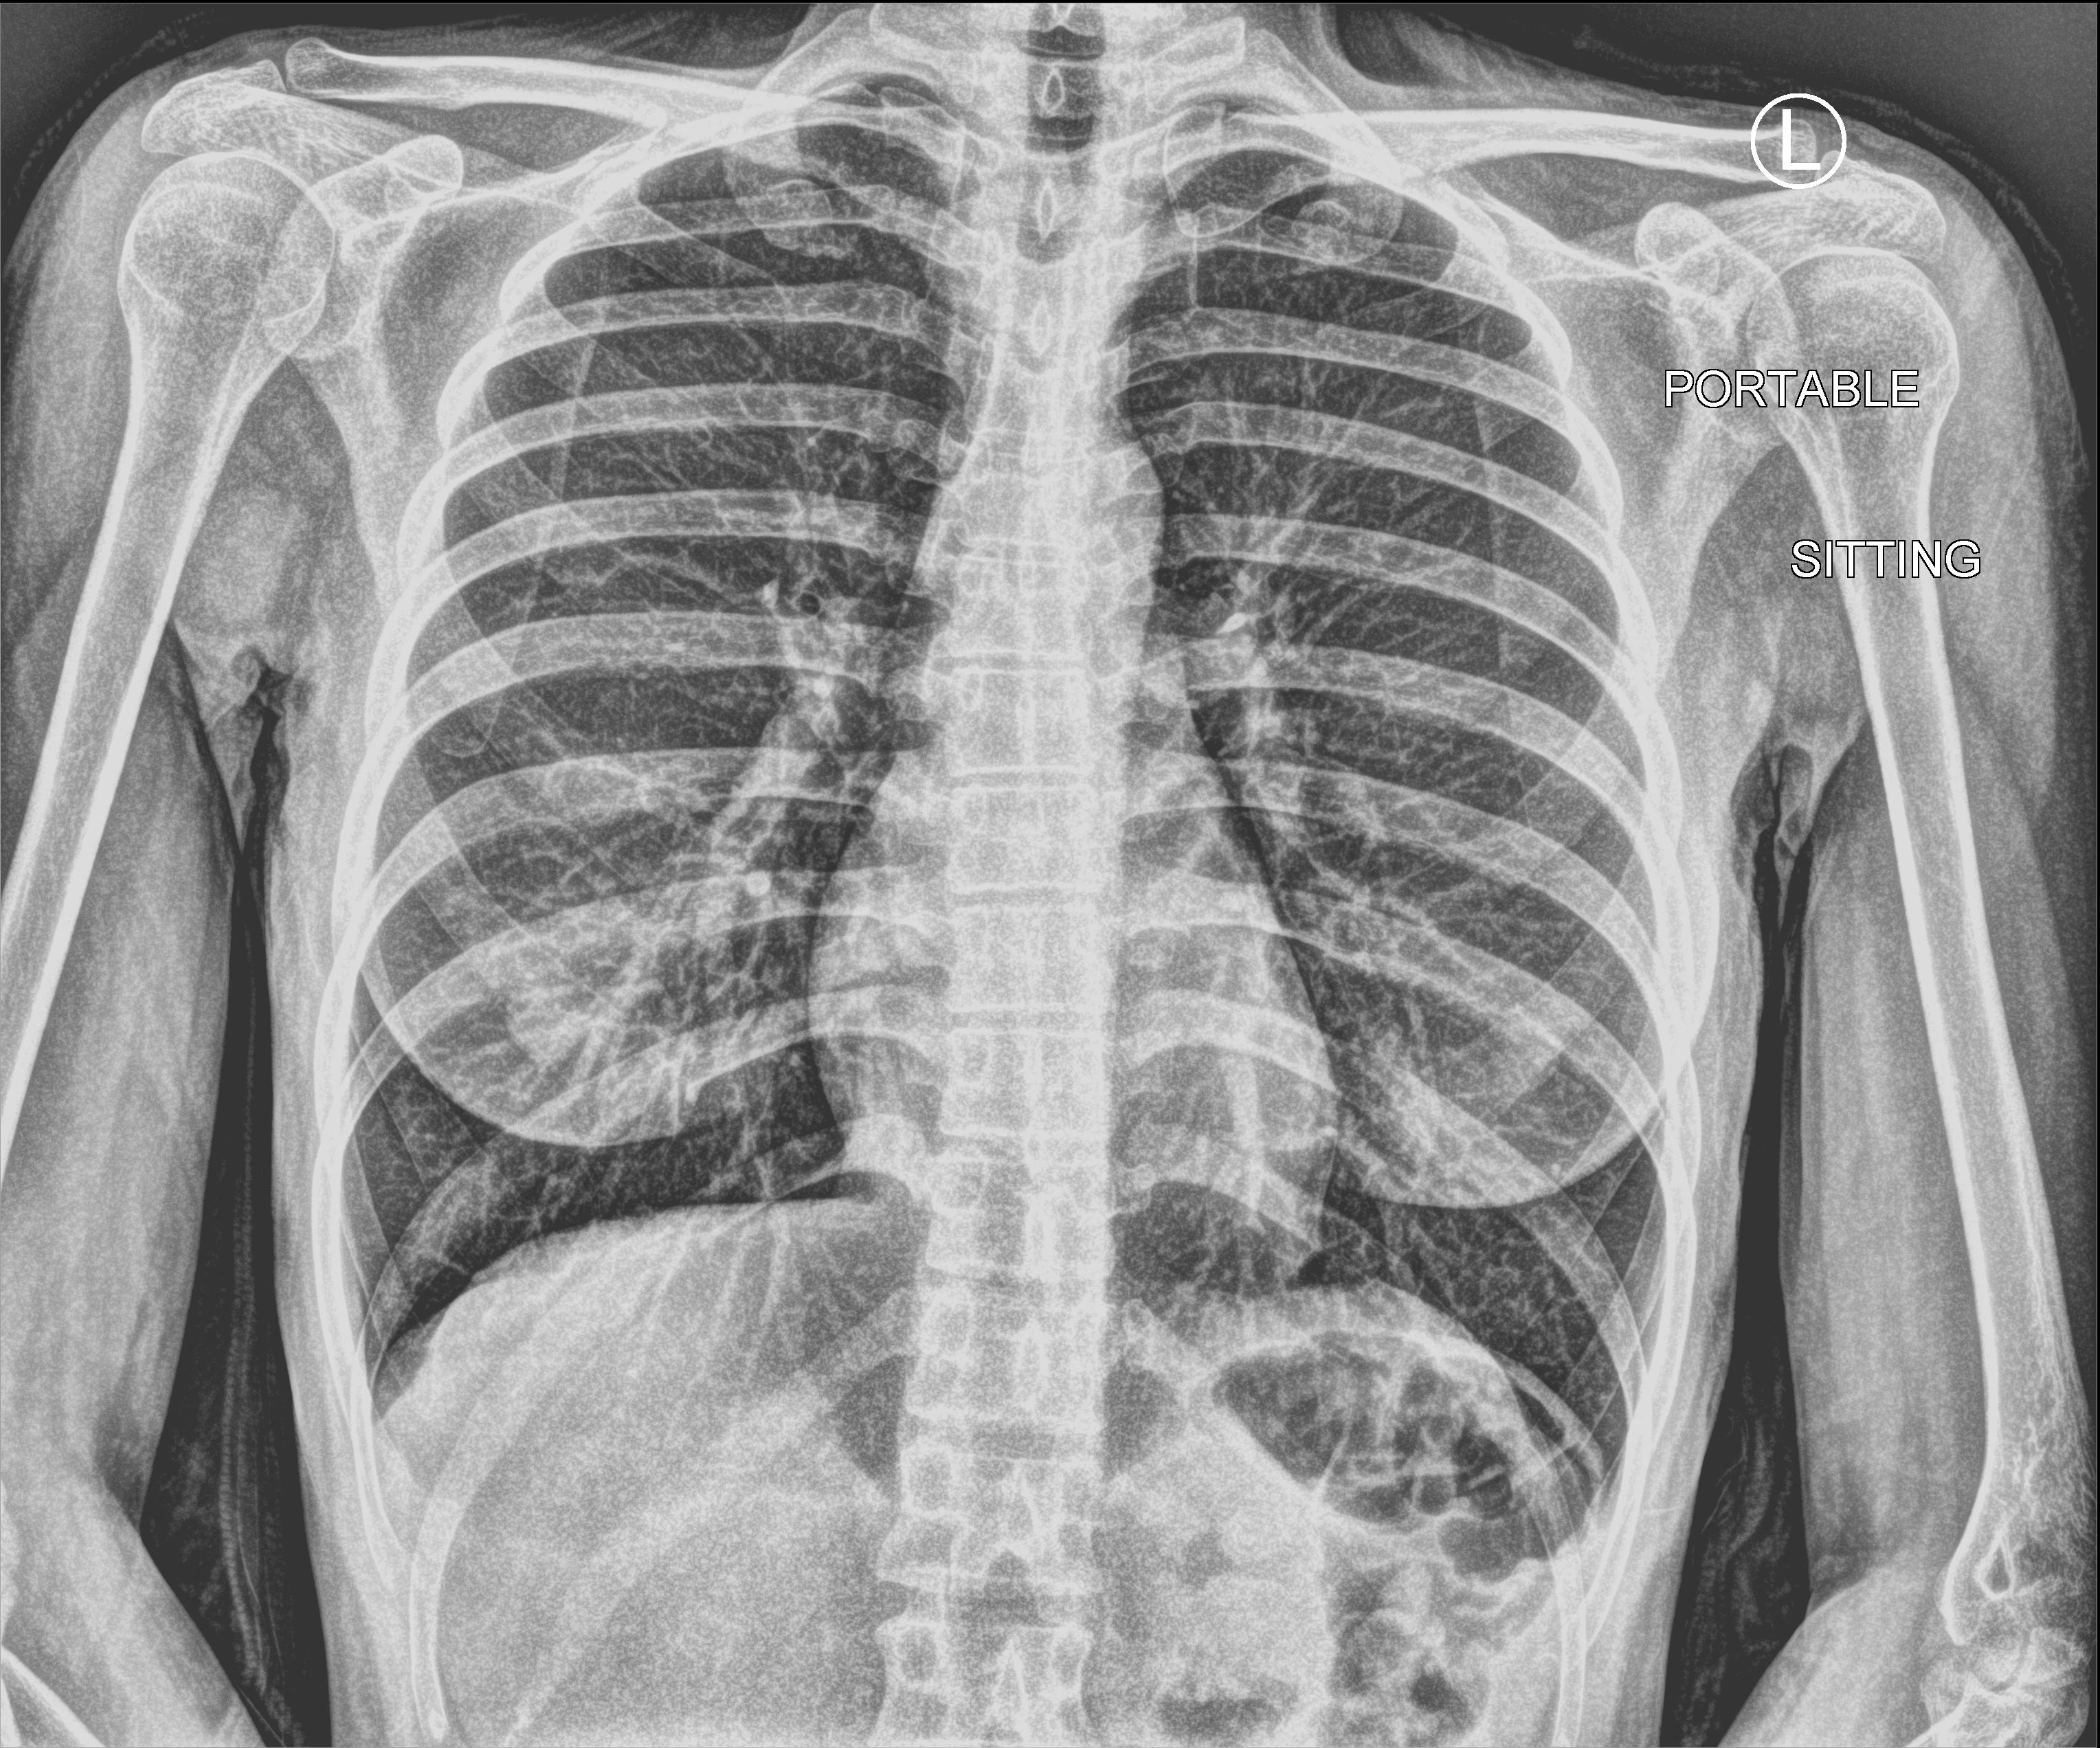
Portable chest radiograph; anteroposterior (AP) projection. Female patient hospitalised with COVID-19, age 18–59 years.
Hospital-stay facts (about this admission, not read from this image; timing relative to this image not recorded):
- admitted to intensive care during this hospital stay: no
- mechanically ventilated during this hospital stay: no